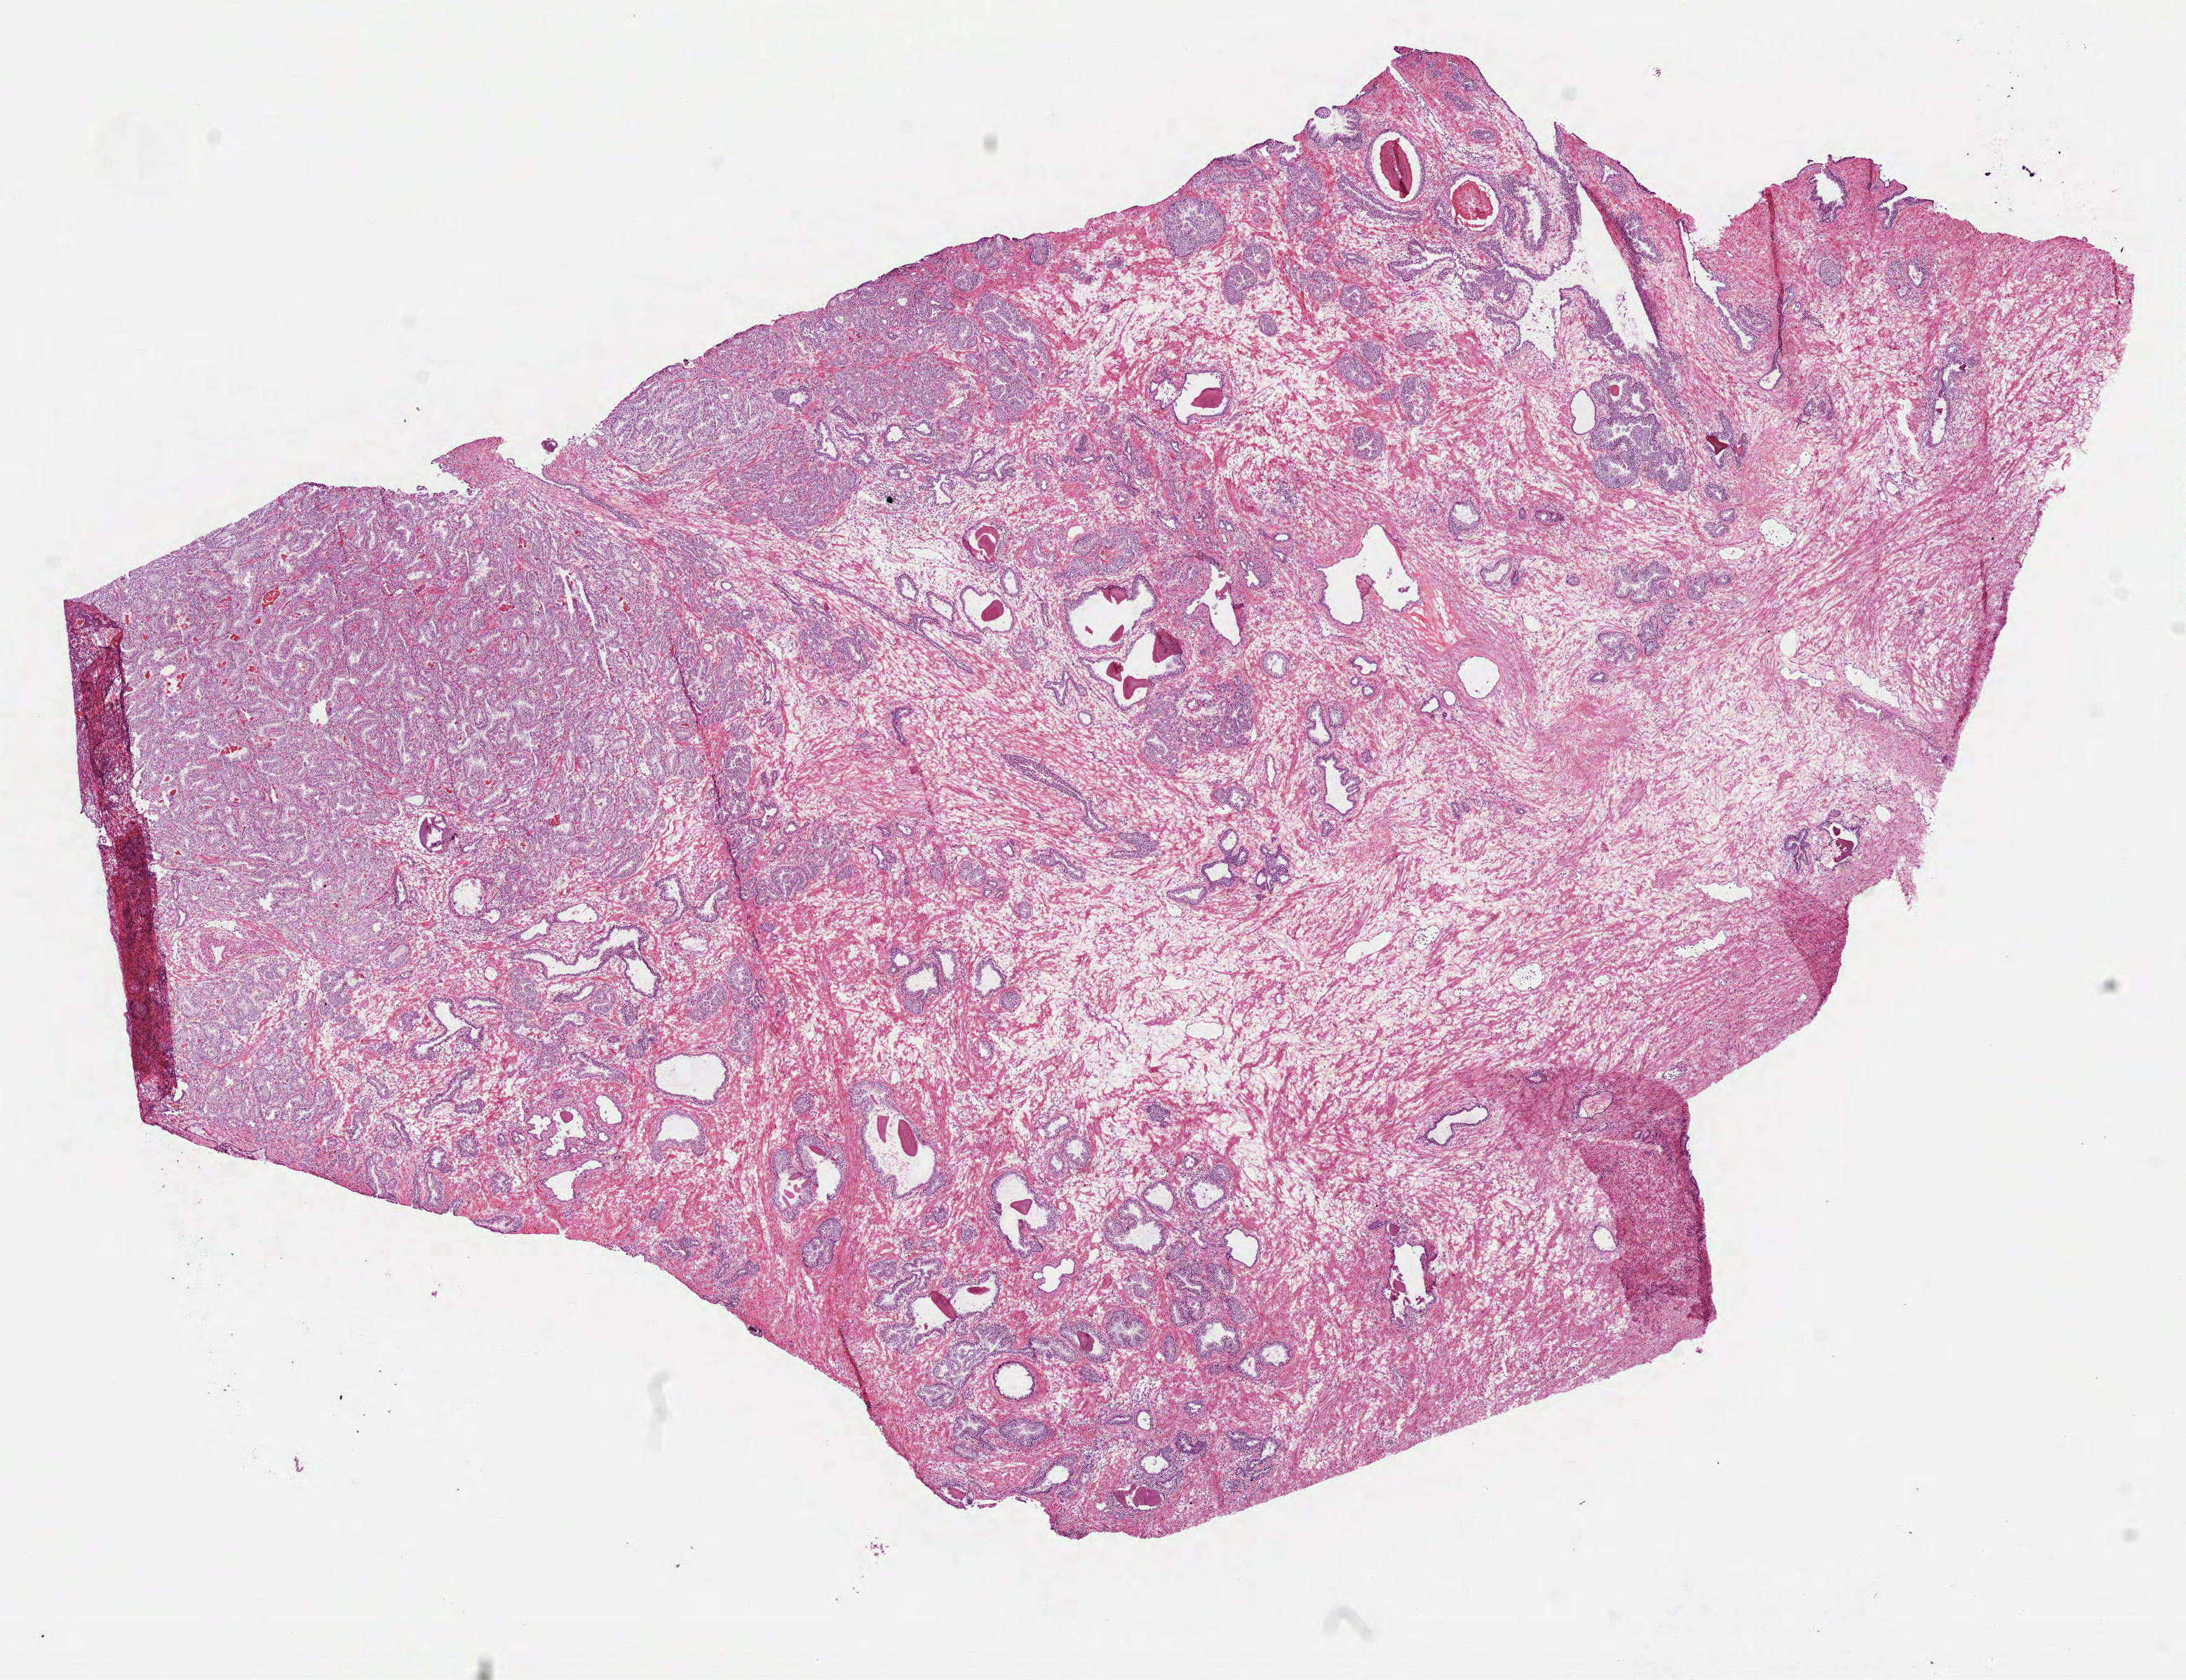
Hematoxylin and eosin (H&E) stained whole-slide image, a low-resolution overview of the entire scanned area, about 12.6 x 9.7 mm (acquisition: 40x scan). Frozen section from the top of the tissue portion. Sample: primary tumour, prostate. Male, age 67 years at initial diagnosis. Gleason score: 7 (3+4). Slide review estimates, as recorded: tumour cells 25%, tumour nuclei 60%, normal cells 25%, stromal cells 50%, necrosis 0%. Infiltration values recorded for this section: lymphocyte infiltration 1%, monocyte infiltration 0%, neutrophil infiltration 0%.
Lymph nodes positive (case pathology): 0 of 11 examined. Diagnosis: Acinar cell carcinoma (prostate gland).